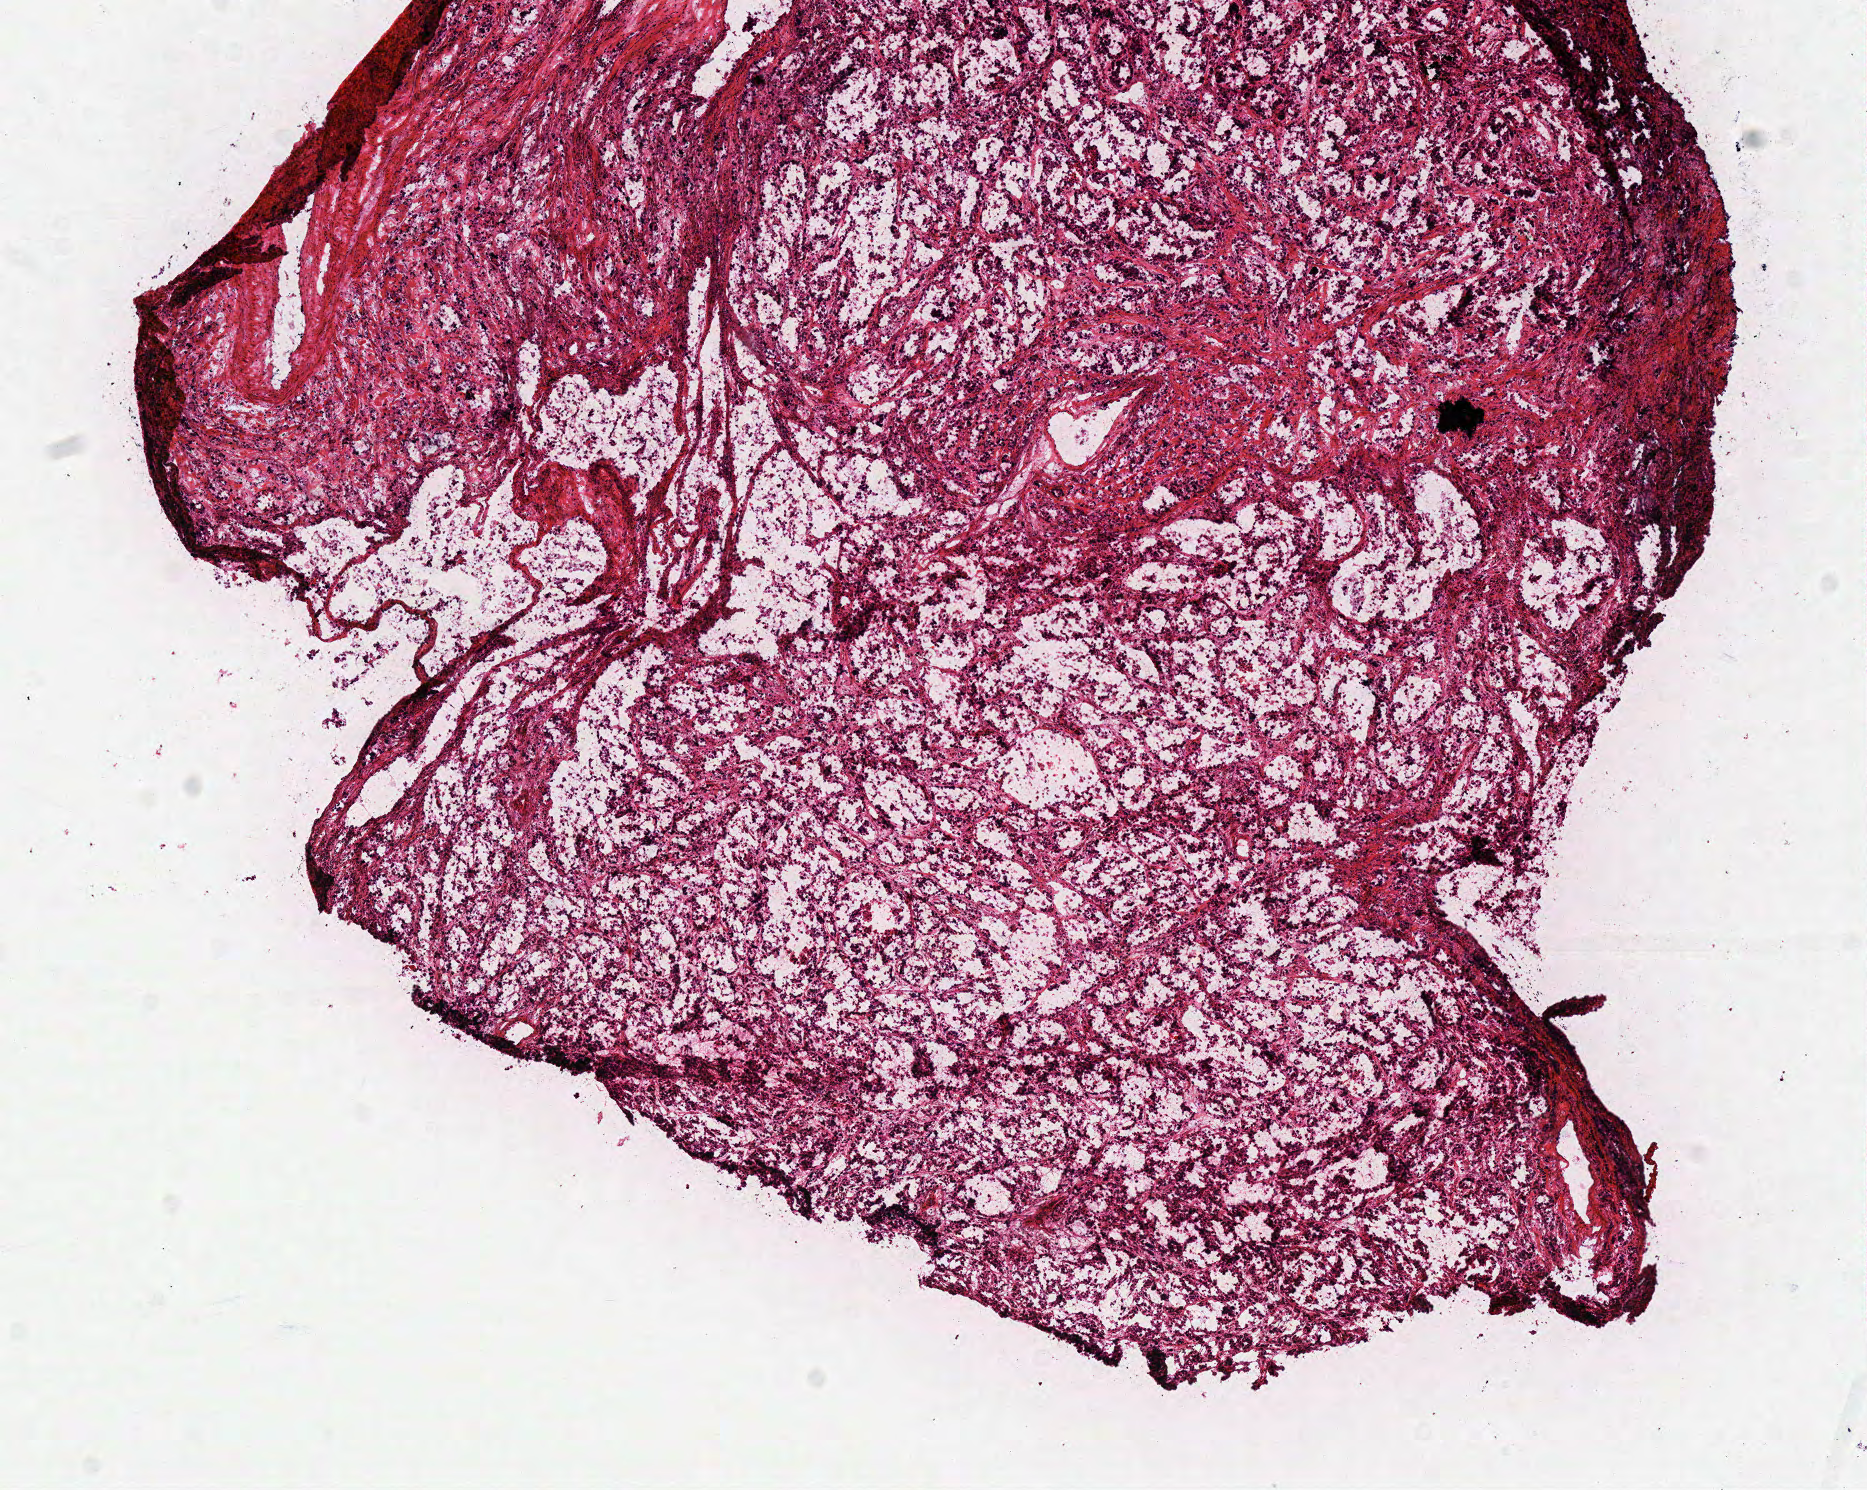
H&E whole-slide image — shown as a low-resolution overview of the whole scanned area (about 7.3 x 5.9 mm, from a 40x scan); frozen section from the top of the tissue portion; primary tumour sample from the lung. Female, age 63 years at initial diagnosis. Pathologist review of this section (percent, as recorded): tumour cells 93%, tumour nuclei 70%, normal cells 0%, stromal cells 5%, necrosis 2%.
Laterality: right. Histologic diagnosis: Adenocarcinoma with mixed subtypes (upper lobe, lung). AJCC pathologic stage: IA (7th edition).